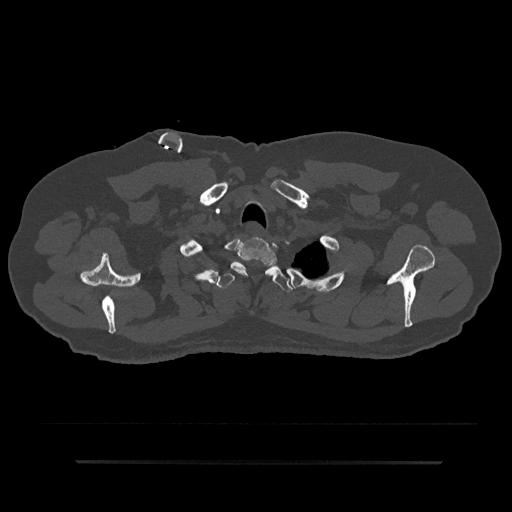
CT including the spine, one axial slice. Position 719 of 797 along the scan axis. Reconstruction kernel Br40s/3. 120 kVp. Bone window (W 1800 / L 400 HU). 0.5 mm slice thickness. 512 × 512 image matrix, field of view 464 × 464 mm. Patient: male, 59 years. Case-level facts recorded for this patient, not image findings: primary cancer: bile ducts.
Outlined on this slice (semi-automatically segmented with operator editing):
- T1 vertebra: box from (x=231, y=237) to (x=278, y=276) px
- T2 vertebra: (x=215, y=263)–(x=293, y=292)